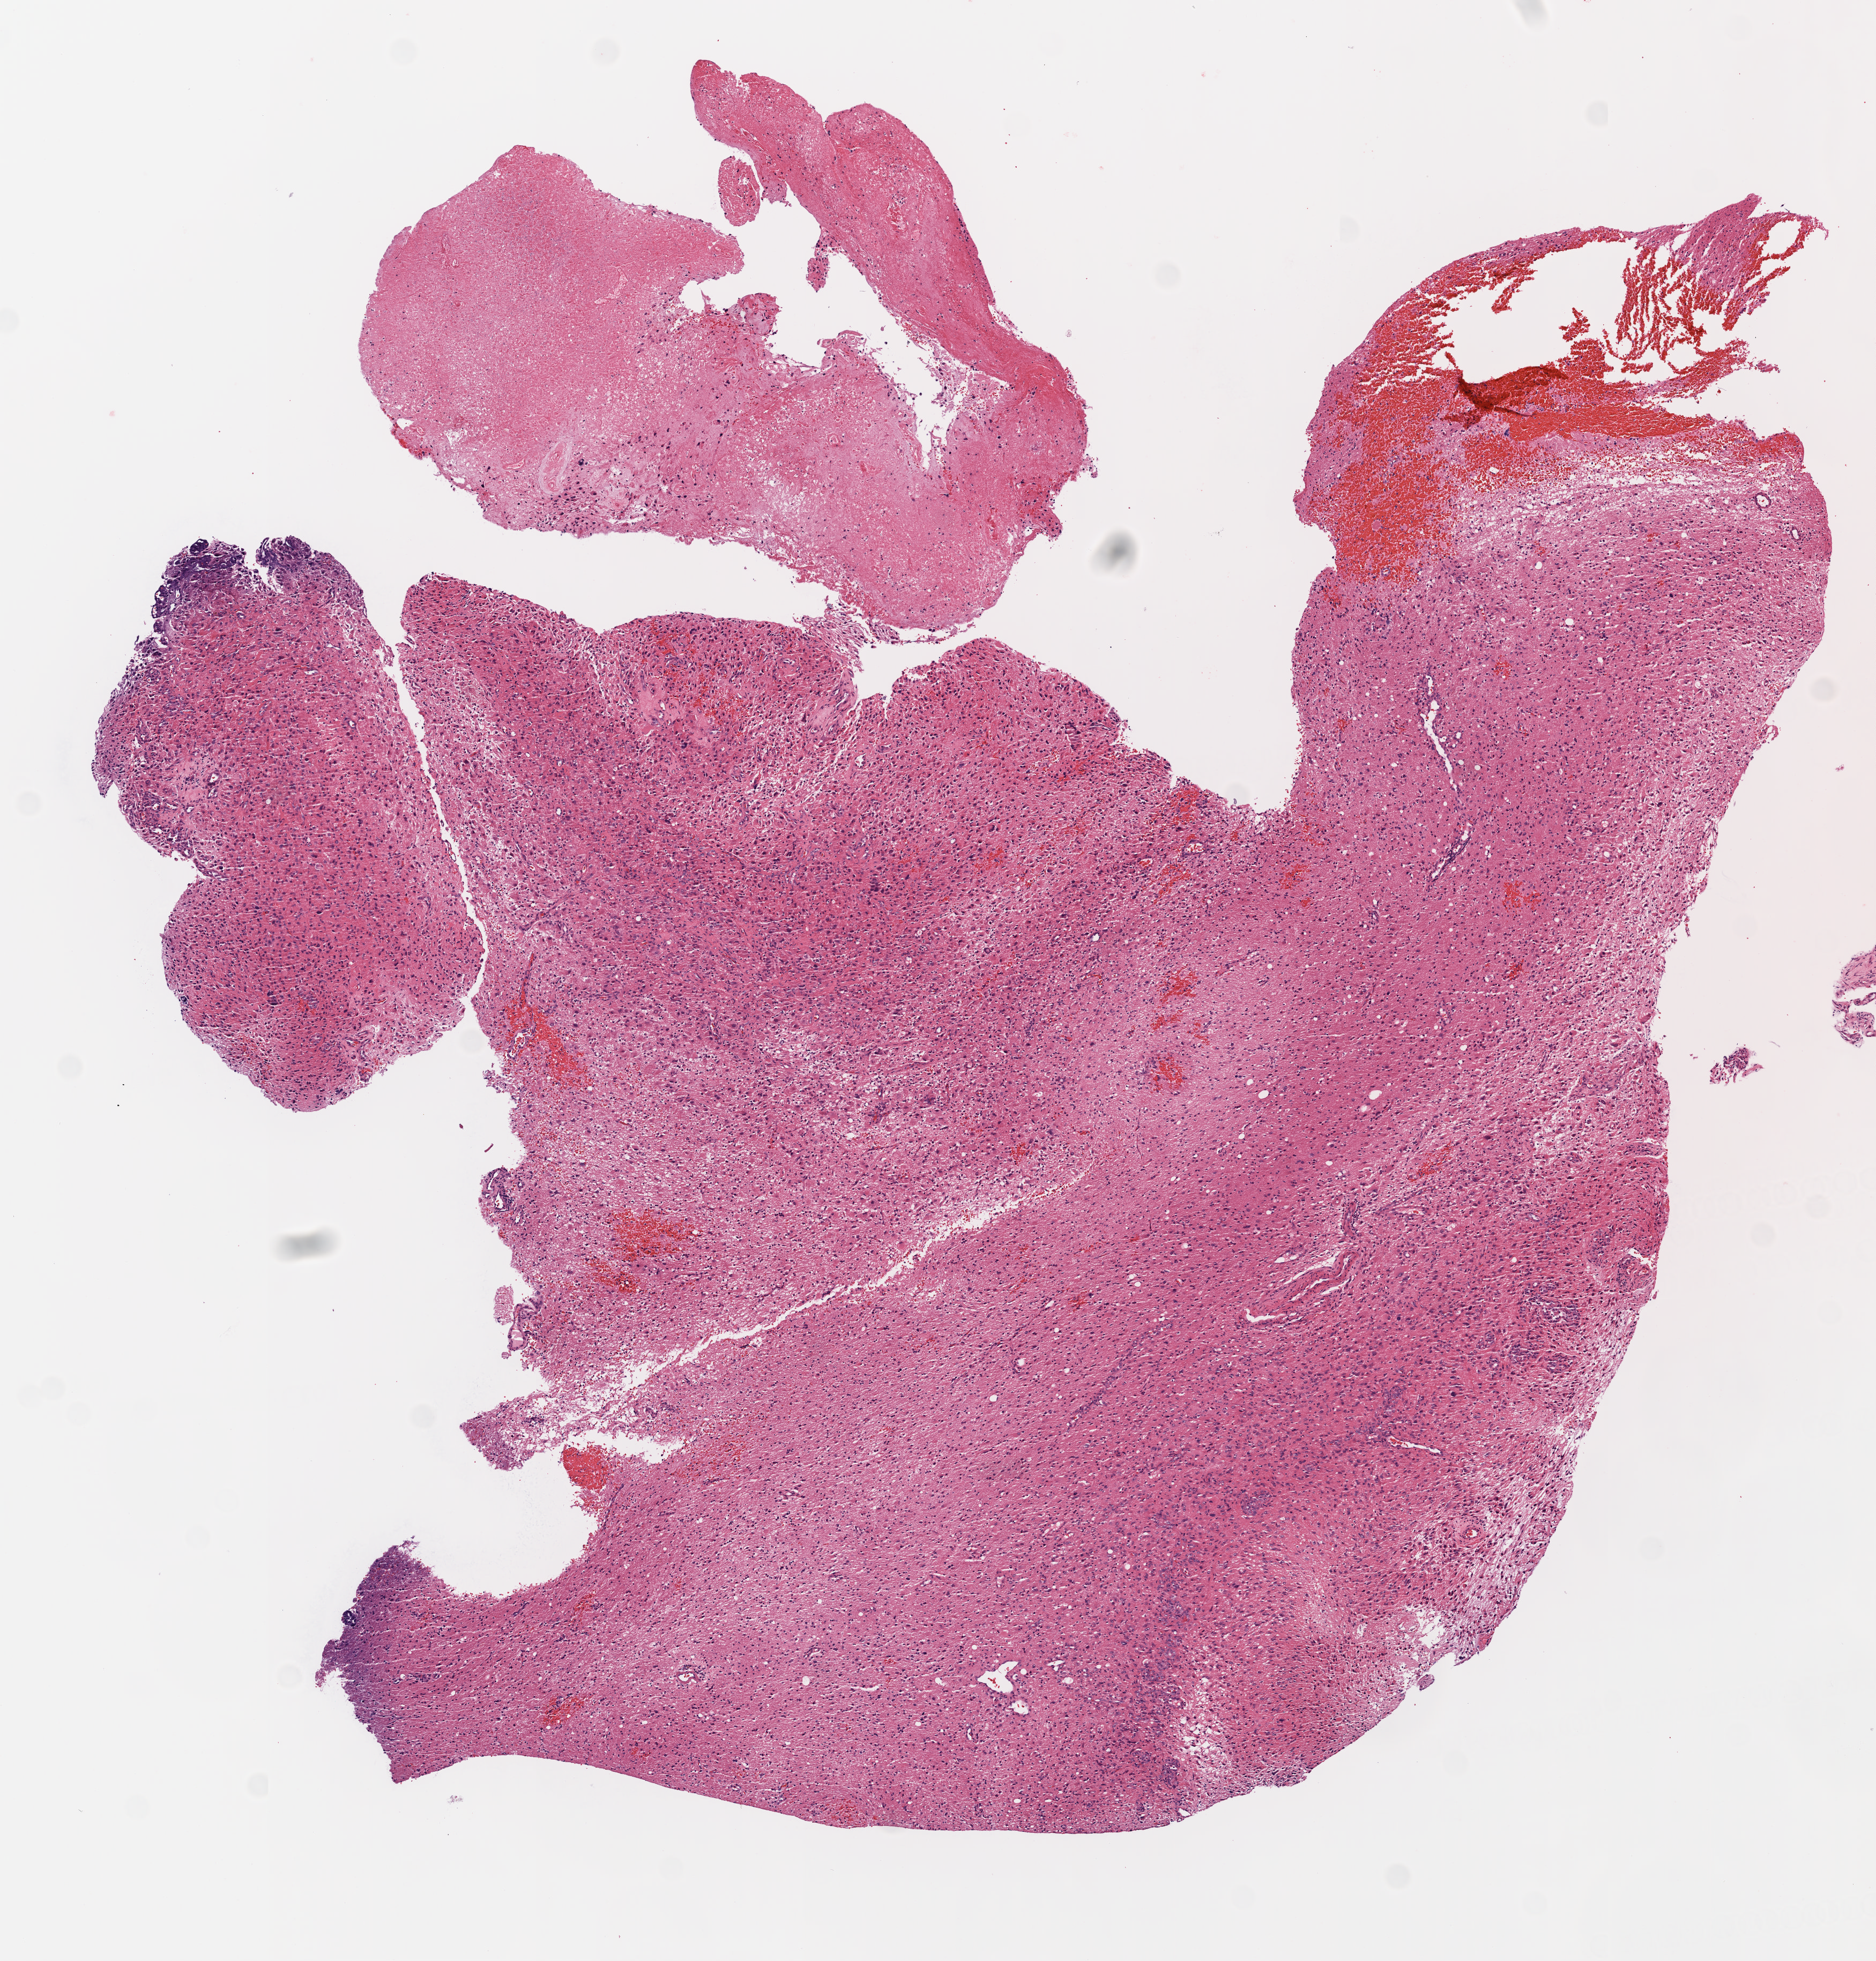
Whole-slide histology image, H&E-stained, low-resolution overview of the scanned area, about 7.0 x 7.3 mm (slide scanned at 20x). FFPE section. Brain, primary tumour sample. Male, age 69 years at initial diagnosis.
Diagnosis: Glioblastoma.